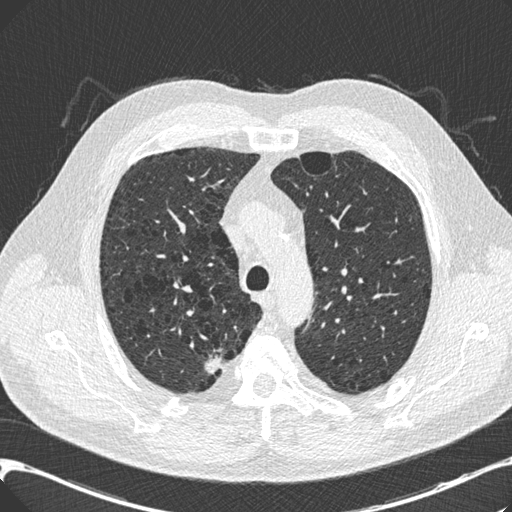
Low-dose screening chest CT, one axial slice. Slice 149 of 197 in the series (ordered by position). Reconstruction kernel B30f. 120 kVp. Lung window (W 1500 / L -600 HU). 0.75 mm slice thickness. 512 × 512 image matrix, field of view 367 × 367 mm.
Structures marked on this image (outlined manually by an expert reader):
- lesion 1 (tumor, upper lobe of right lung): bounding box (x1, y1, x2, y2) in pixels: (205, 354, 222, 374)